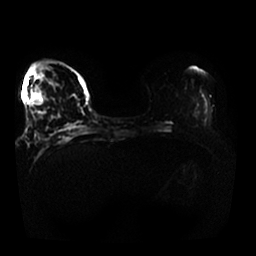
Breast MRI, one axial slice; position 10 of 25 along the scan axis; diffusion-weighted series; image 2 of 4 stored at this slice position (different b-values; order by instance number); 1.5 T; 4 mm slice thickness; 256 × 256 image matrix. Female patient.
Annotated regions visible in this slice (expert manual segmentation):
- tumour on diffusion-weighted imaging: bounding box (x1, y1, x2, y2) in pixels: (34, 63, 50, 106)